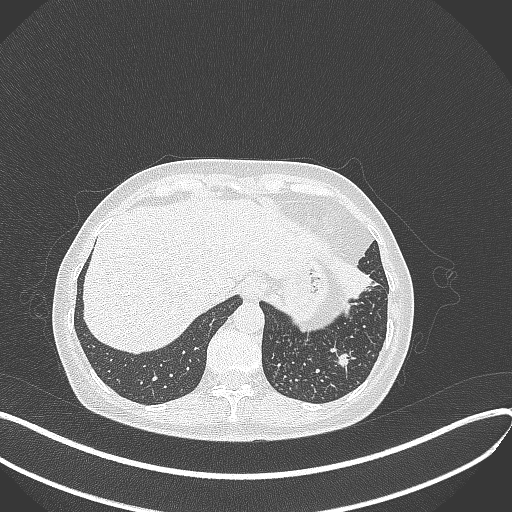
Chest CT, one axial slice. Slice 78 of 429 in the series (ordered by position). 100 kVp. Lung window (W 1500 / L -600 HU). 1 mm slice thickness. 512 × 512 image matrix. Patient: female, 63 years. From the clinical record (not read from this slice): clinical TNM (as recorded): T1b N0 M0; histopathological grade: G2-3.
Annotated regions visible in this slice (bounding box drawn by a radiologist):
- lung tumour (recorded histology: adenocarcinoma): box from (x=338, y=261) to (x=377, y=305) px